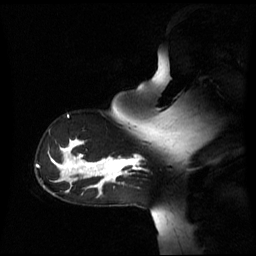
Breast MRI (dynamic contrast-enhanced), one sagittal slice; position 45 of 60 along the scan axis; dynamic contrast-enhanced series, image 2 of 3 at this slice position (ordered by acquisition); 1.5 T; TE 4.2 ms, TR 8.4 ms; 256 × 256 image matrix, field of view 270 × 270 mm. Female patient, age 39 years. Case-level facts recorded for this patient, not image findings: setting: breast cancer imaged before/during neoadjuvant chemotherapy; receptor status: triple-negative.
Structures marked on this image (semi-automatic segmentation, software-assisted and operator-edited):
- analysis volume of interest (the breast-tissue region the enhancement analysis was run in; not a lesion): box from (x=105, y=157) to (x=139, y=179) px
- tumour enhancement mask (voxels above the 70 % enhancement threshold inside the analysis volume of interest): (x=105, y=157)–(x=139, y=179)